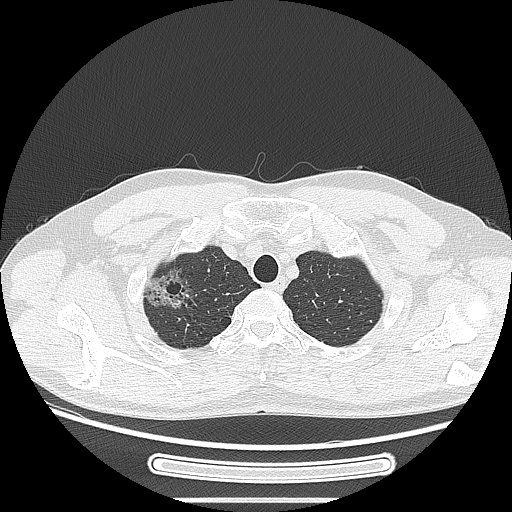
Chest CT, one axial slice; position 230 of 269 along the scan axis; 120 kVp; lung window (W 1500 / L -600 HU); 1.25 mm slice thickness; 512 × 512 image matrix, field of view 382 × 382 mm. Male patient, age 53 years. From the clinical record (not read from this slice): clinical TNM (as recorded): T1c N0 M0.
Annotated regions visible in this slice (rectangle marked by the reading radiologist):
- lung tumour (recorded histology: adenocarcinoma): bounding box <138,262,202,318> (left, top, right, bottom; pixels)